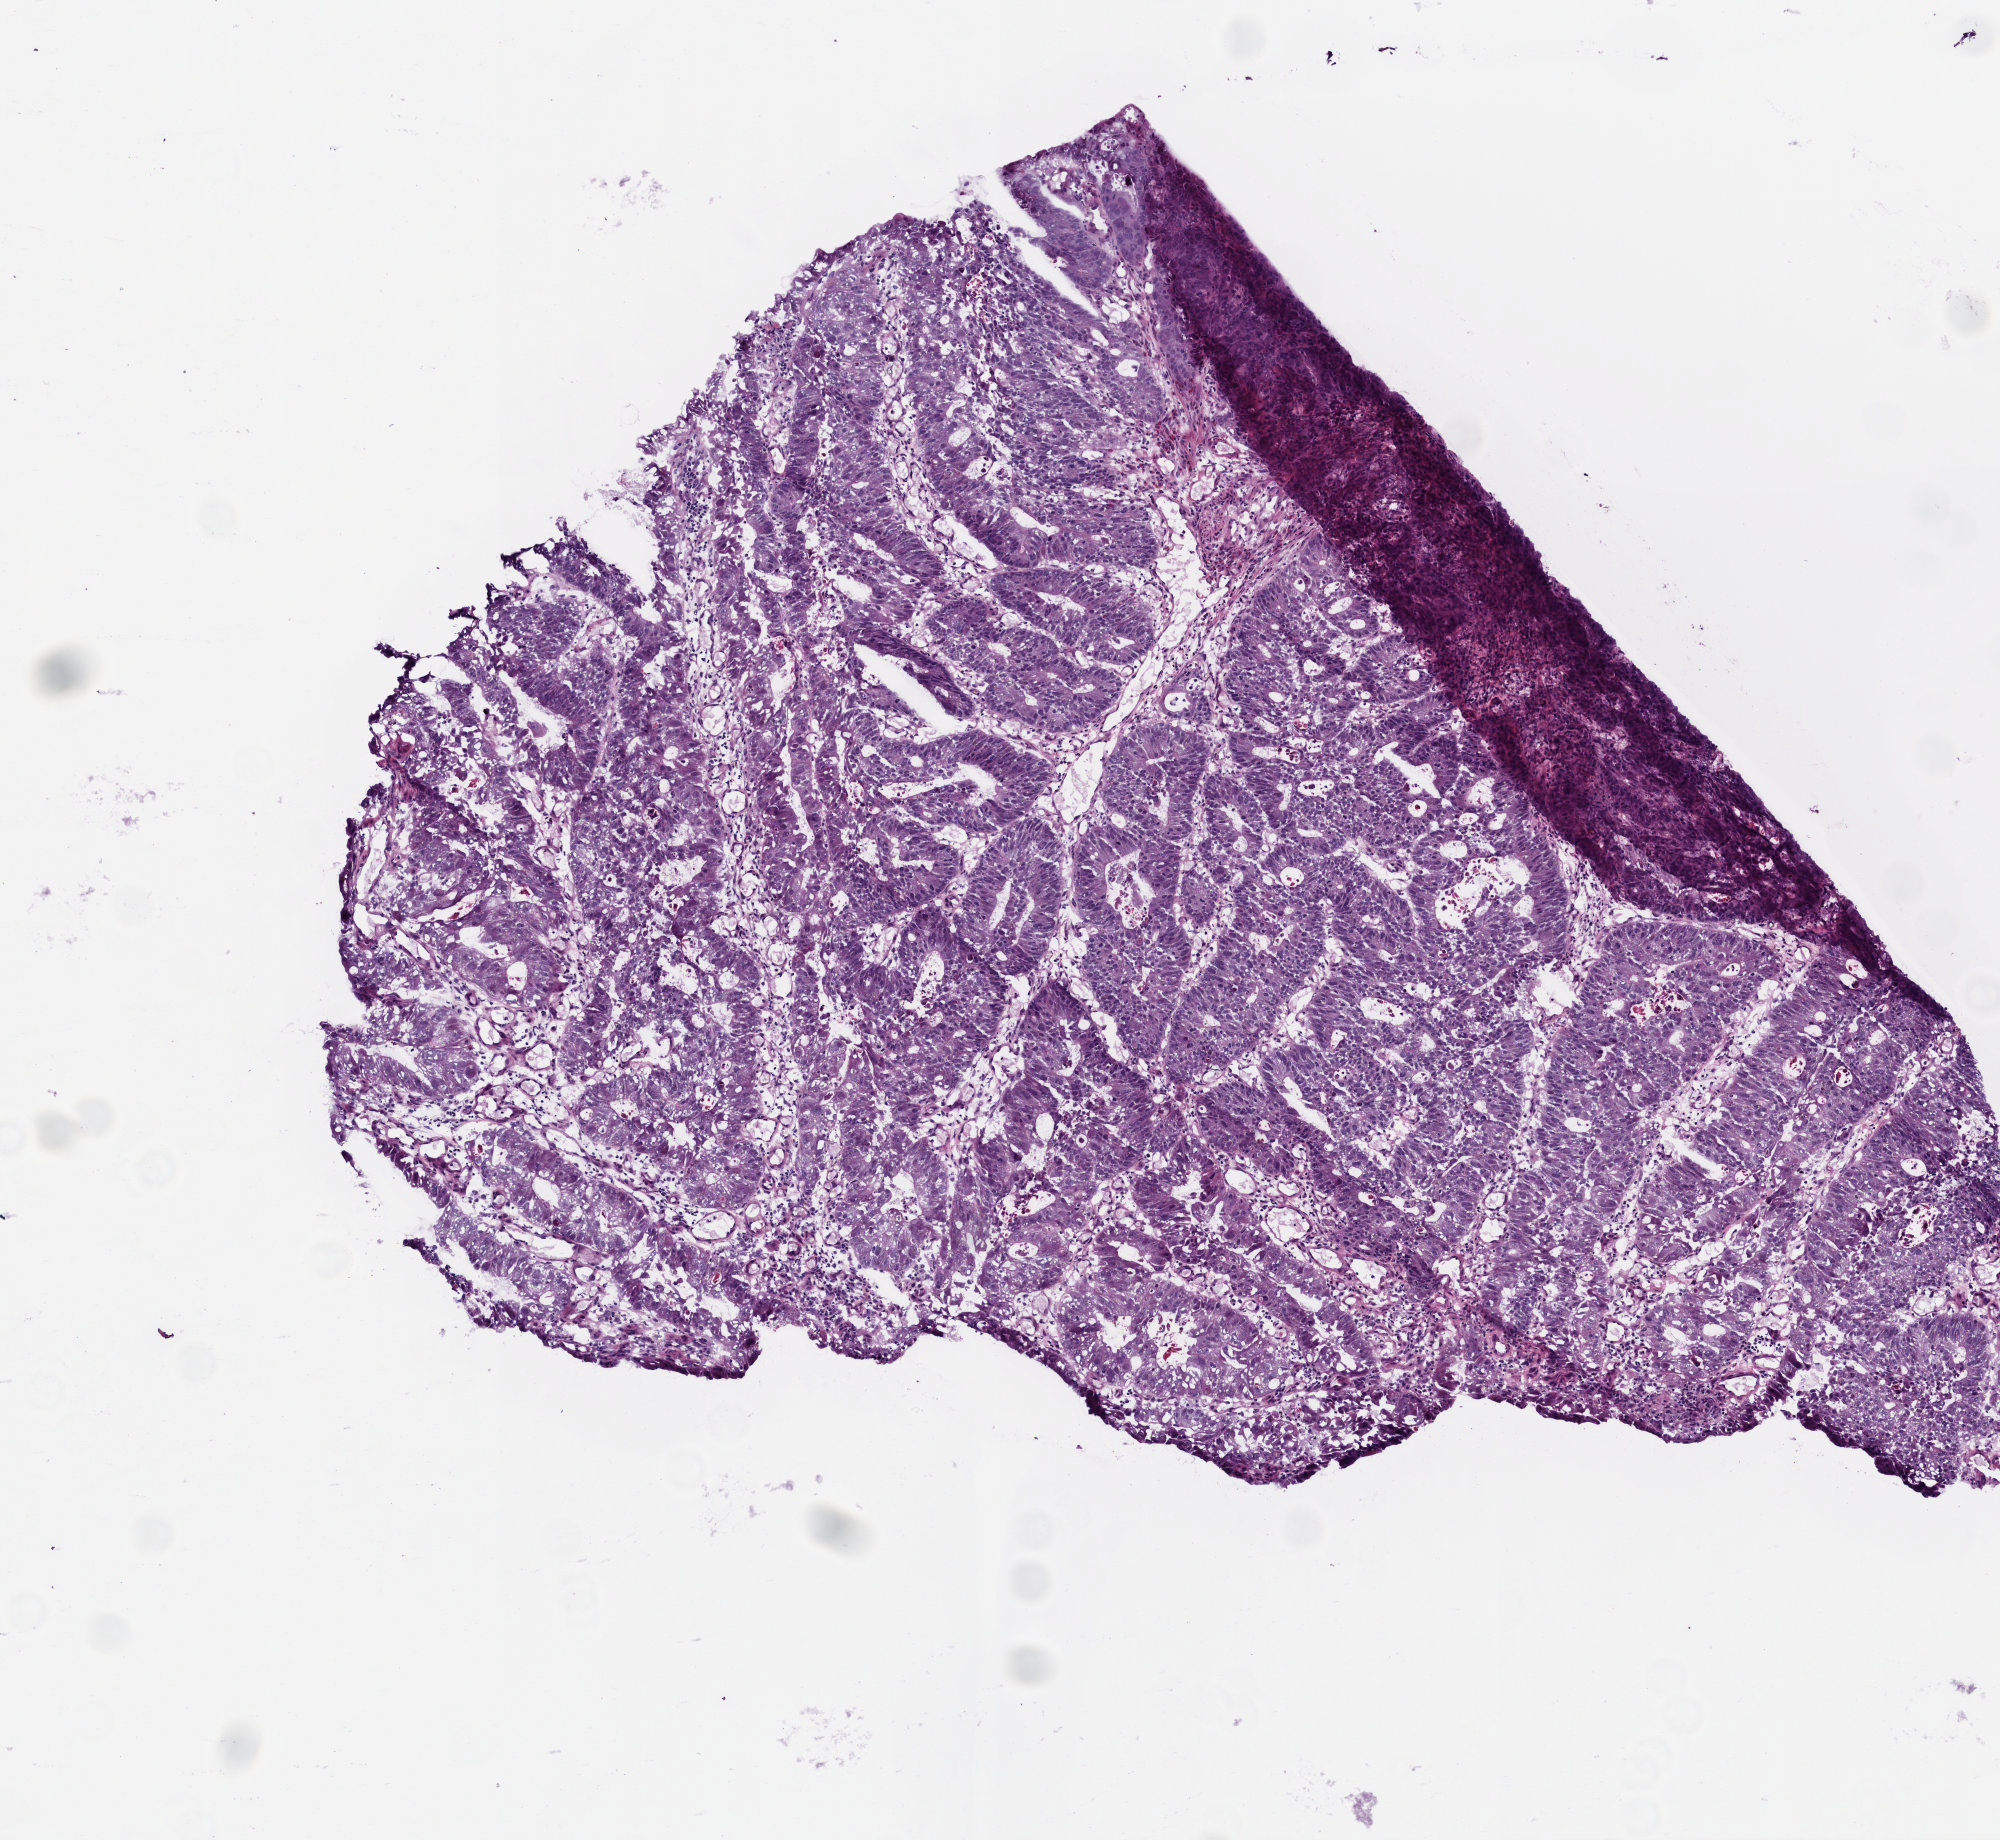
H&E-stained whole-slide image, low-resolution overview of the scanned area, about 4.0 x 3.7 mm (slide scanned at 20x); frozen section; primary tumour sample from the rectum. Female, age 63 years at initial diagnosis. Slide review estimates, as recorded: tumour cells 83%, tumour nuclei 75%, normal cells 0%, stromal cells 12%, necrosis 5%.
Lymph nodes positive (case pathology): 0 of 34 examined. AJCC pathologic stage: I. Histologic diagnosis: Adenocarcinoma, NOS.